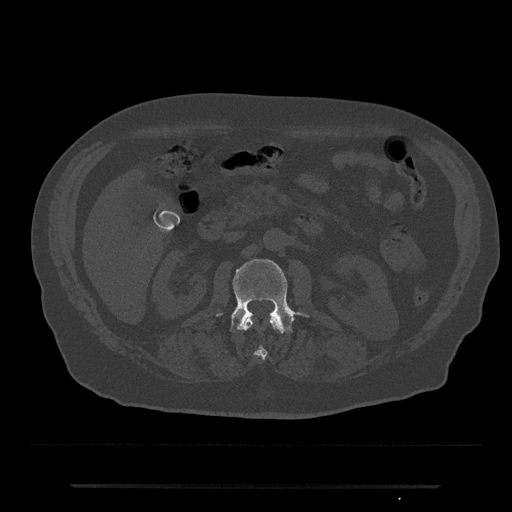
CT including the spine, one axial slice; slice 489 of 797 in the series (ordered by position); reconstruction kernel Br40s/3; 120 kVp; bone window (W 1800 / L 400 HU); 0.5 mm slice thickness; 512 × 512 image matrix, field of view 434 × 434 mm. Male patient, age 80 years. From the clinical record (not read from this slice): primary cancer: prostate; vertebrae with lytic lesions (as recorded): L1, T11.
Annotated regions visible in this slice (semi-automatic segmentation, software-assisted and operator-edited):
- L1 vertebra: bounding box (x1, y1, x2, y2) in pixels: (242, 317, 282, 359)
- L2 vertebra: (216, 259, 310, 333)